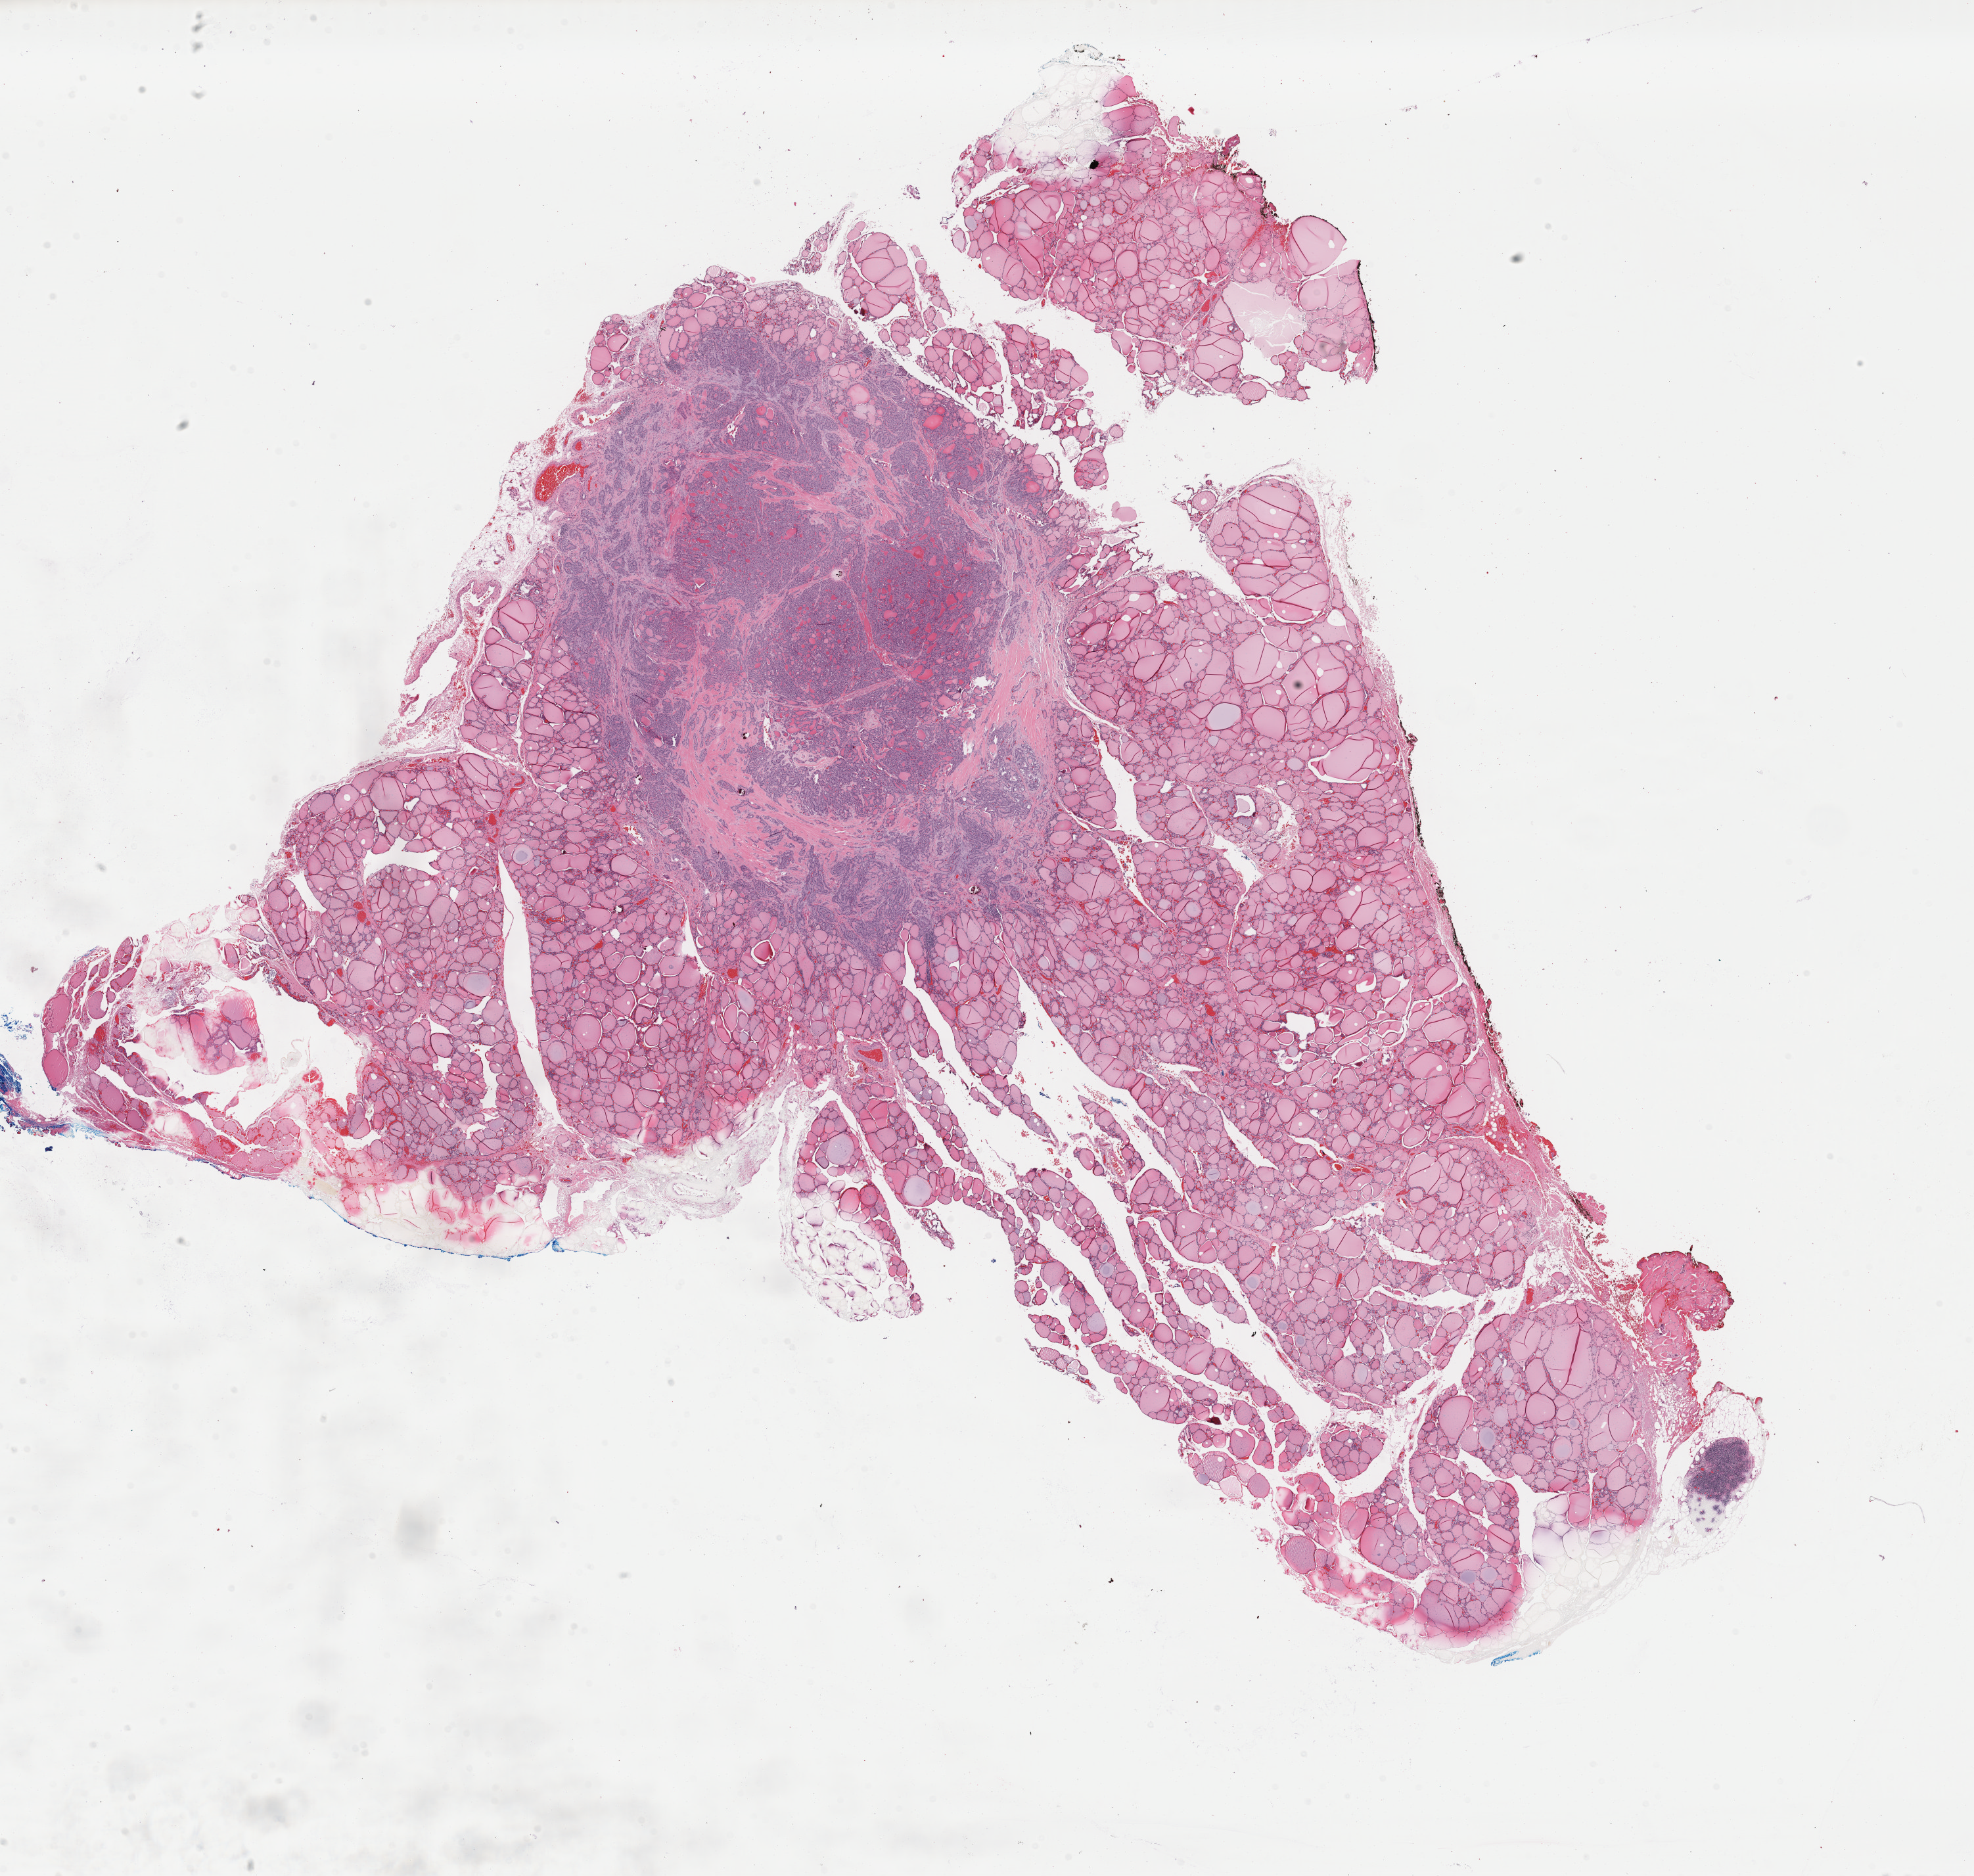
Whole-slide histology image, H&E-stained — a low-resolution overview of the entire scanned area, about 23.7 x 22.5 mm; formalin-fixed paraffin-embedded (FFPE) diagnostic section; sample: primary tumour, thyroid. Patient: female, age at initial diagnosis 48 years.
Pathologic diagnosis: Papillary carcinoma, columnar cell (thyroid gland).